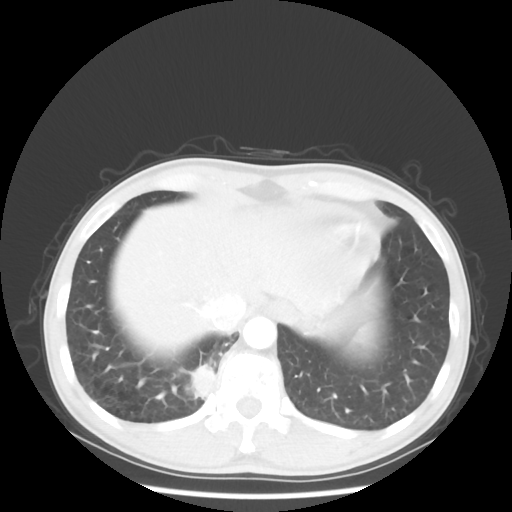
Chest CT, one axial slice. Slice 8 of 58 in the series (ordered by position). Reconstruction kernel STANDARD. Lung window (W 1500 / L -600 HU). 5 mm slice thickness. 512 × 512 image matrix. Patient: male, 56 years. From the clinical record (not read from this slice): clinical TNM (as recorded): T2 N1 M1.
Annotated regions visible in this slice (rectangle marked by the reading radiologist):
- lung tumour (recorded histology: adenocarcinoma): bounding box [x1, y1, x2, y2] px = [188, 359, 216, 400]